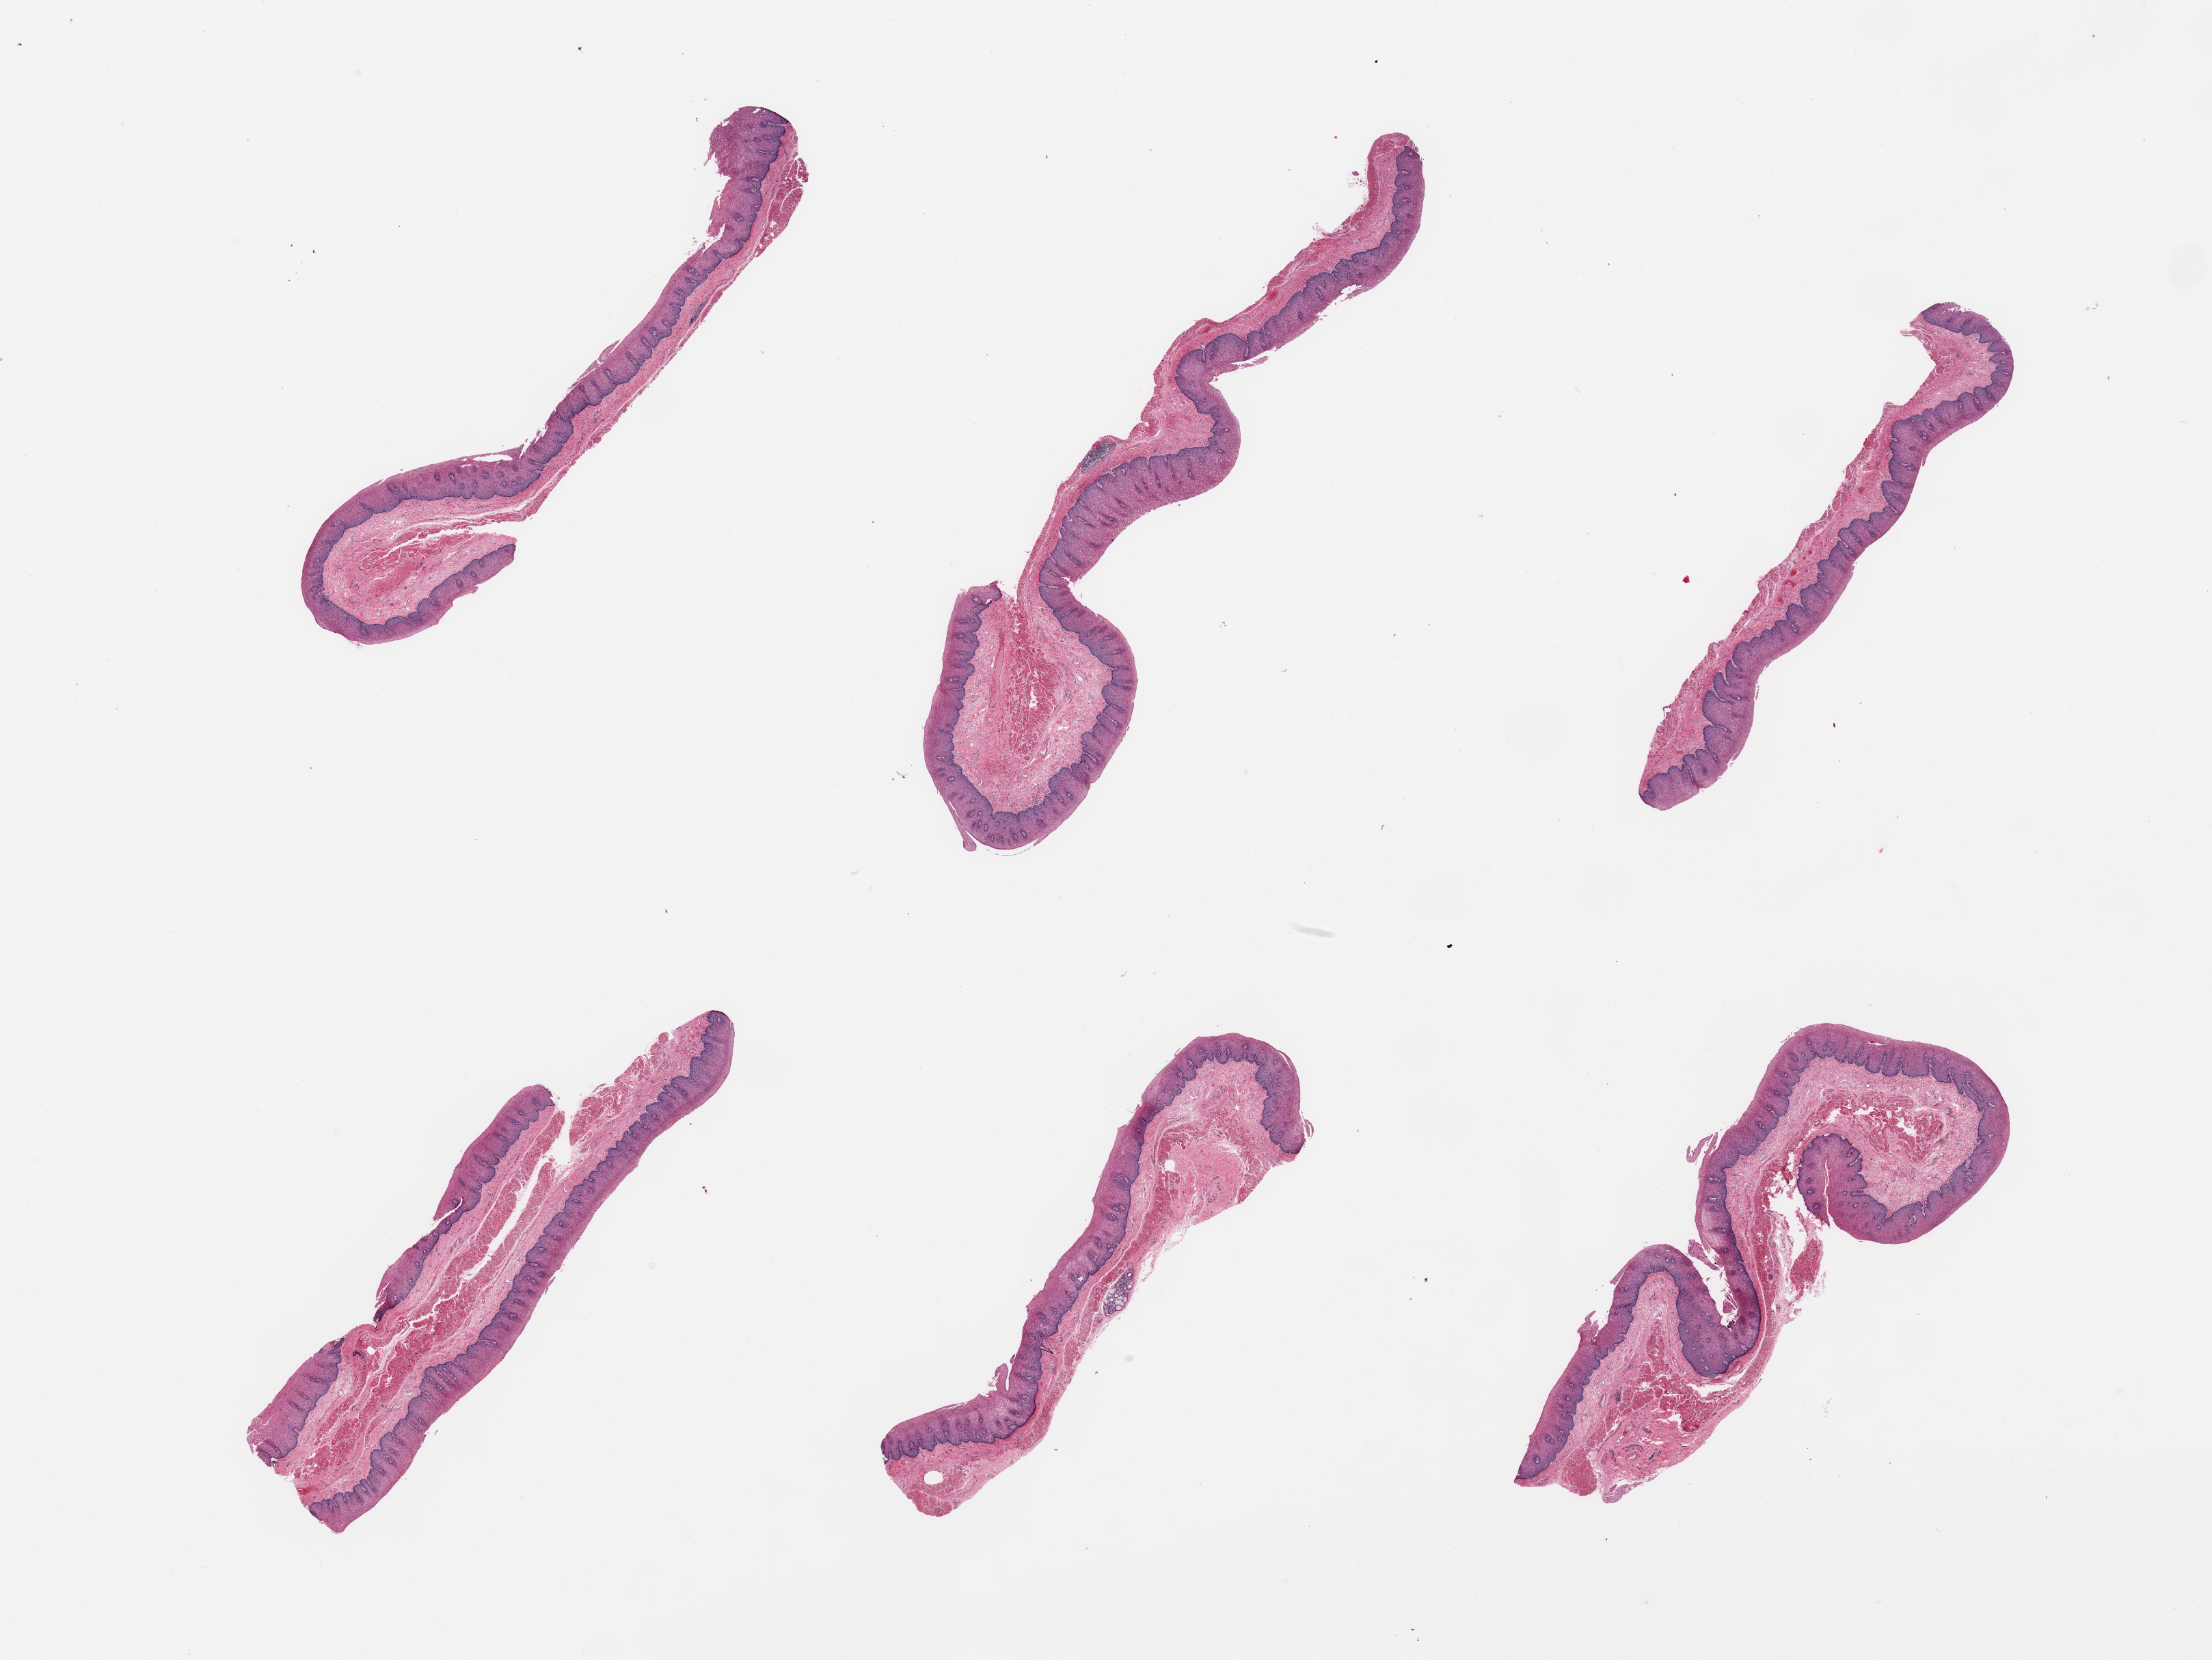
H&E whole-slide image — whole scanned area (about 25.6 x 19.2 mm, slide scanned at 20x) shown as a low-resolution overview. PAXgene-fixed paraffin-embedded (PFPE) section. Target tissue: esophageal mucous membrane. Tissue donor sample.
Review note (as recorded): 6 pieces; well dissected; only 1 small extraneous submucosal gland.